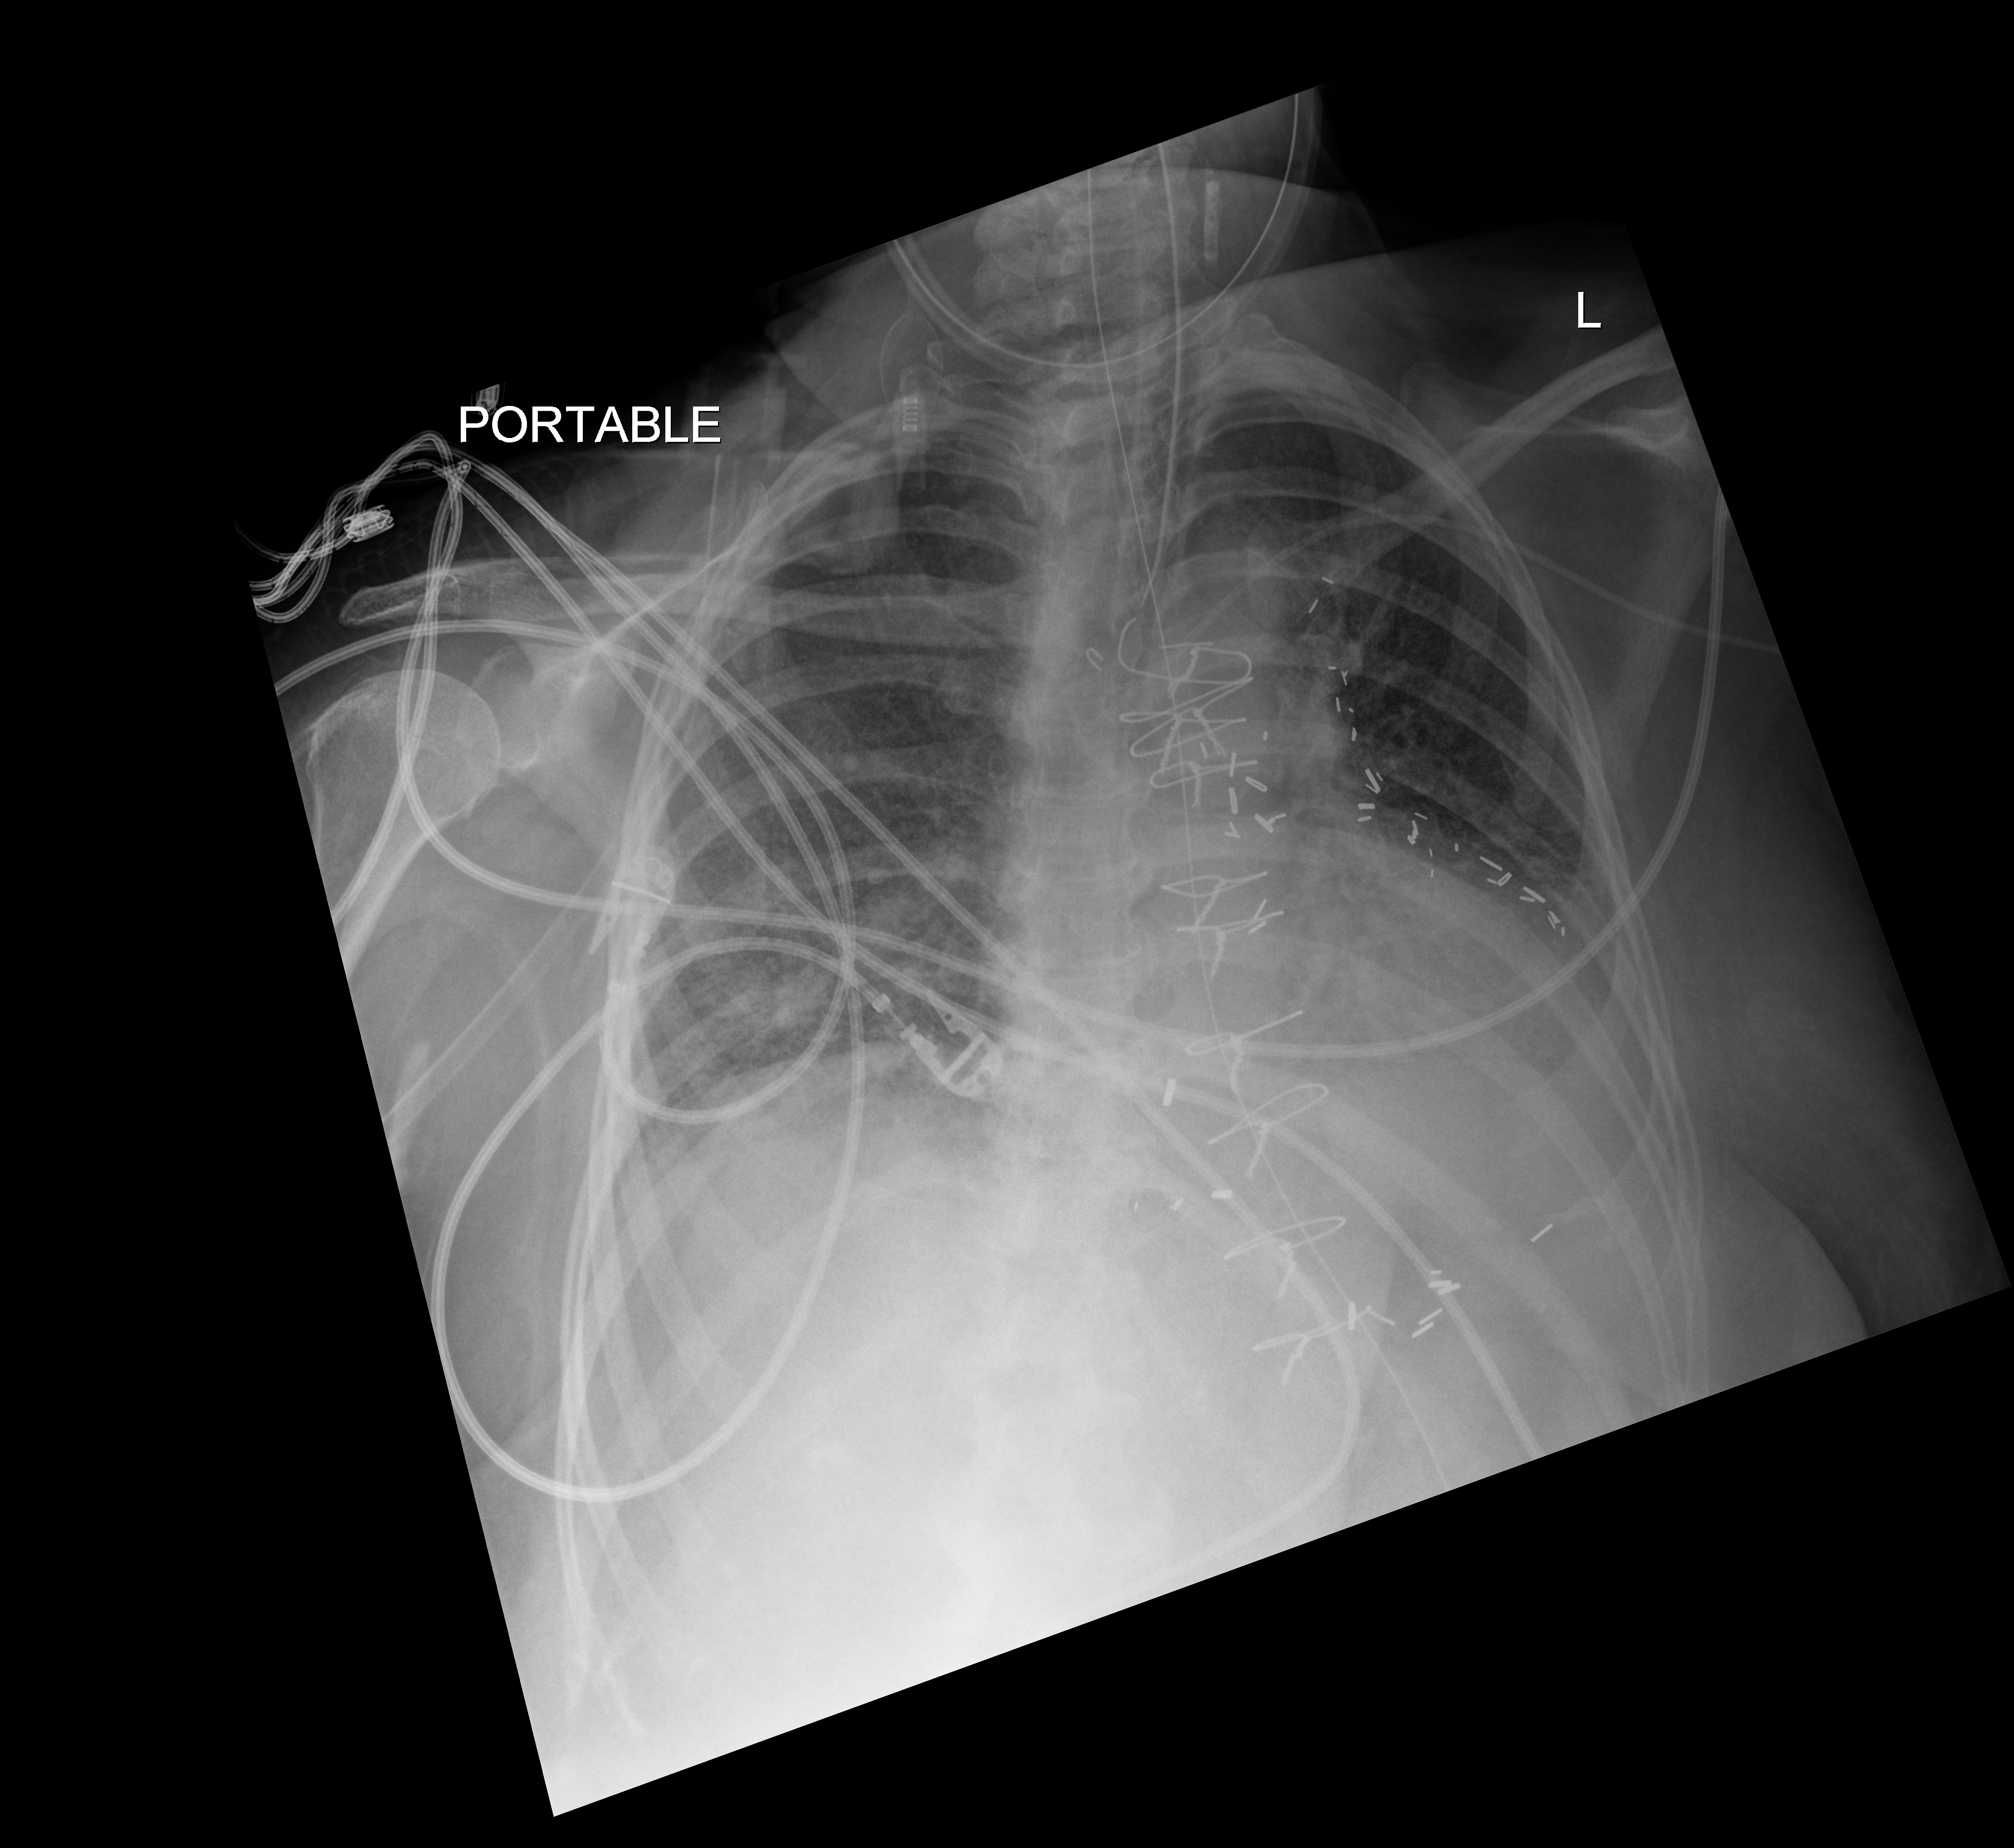
Bedside chest radiograph (digital radiography), anteroposterior (AP) projection. Patient hospitalised with COVID-19; female, aged 60–74 years.
Hospital-stay facts (about this admission, not read from this image; timing relative to this image not recorded):
- length of hospital stay: 25 days
- admitted to intensive care during this hospital stay: yes
- mechanically ventilated during this hospital stay: yes